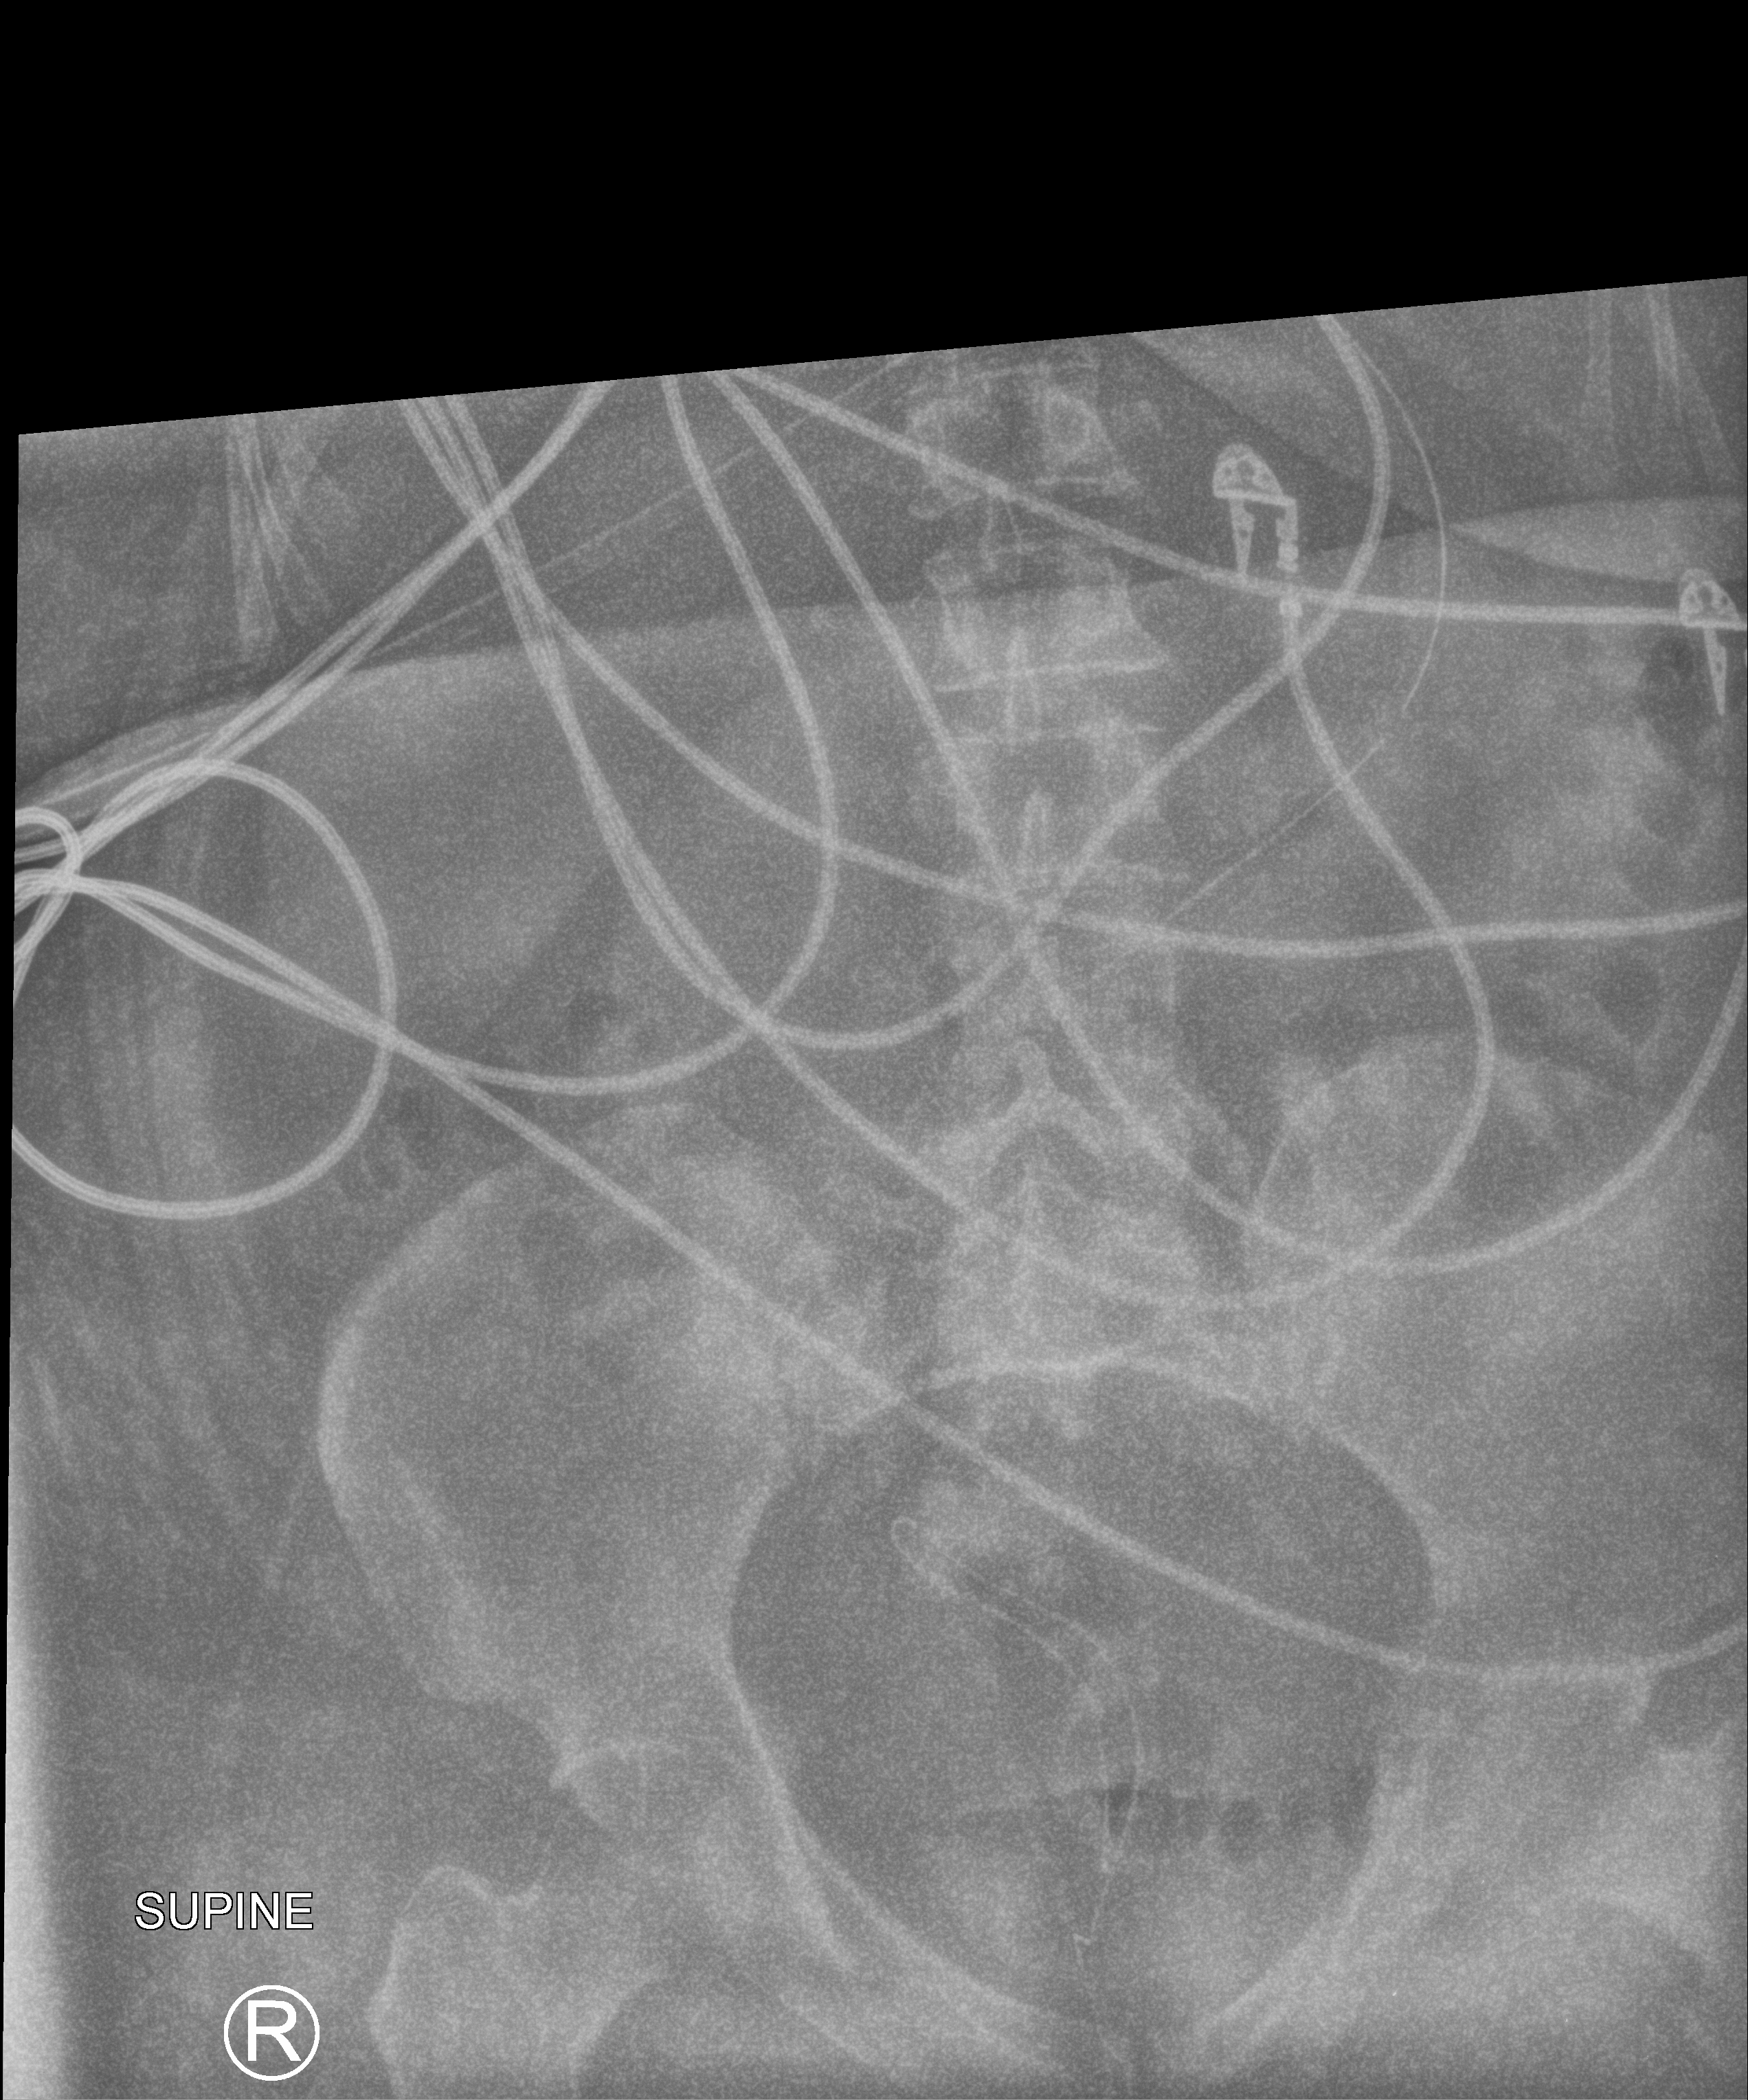
Bedside abdomen radiograph (computed radiography); anteroposterior (AP) projection. Patient hospitalised with COVID-19; female, aged 18–59 years.
Admission-level facts for this patient (not findings on this image; timing relative to this image not recorded): mechanically ventilated during this hospital stay: yes.